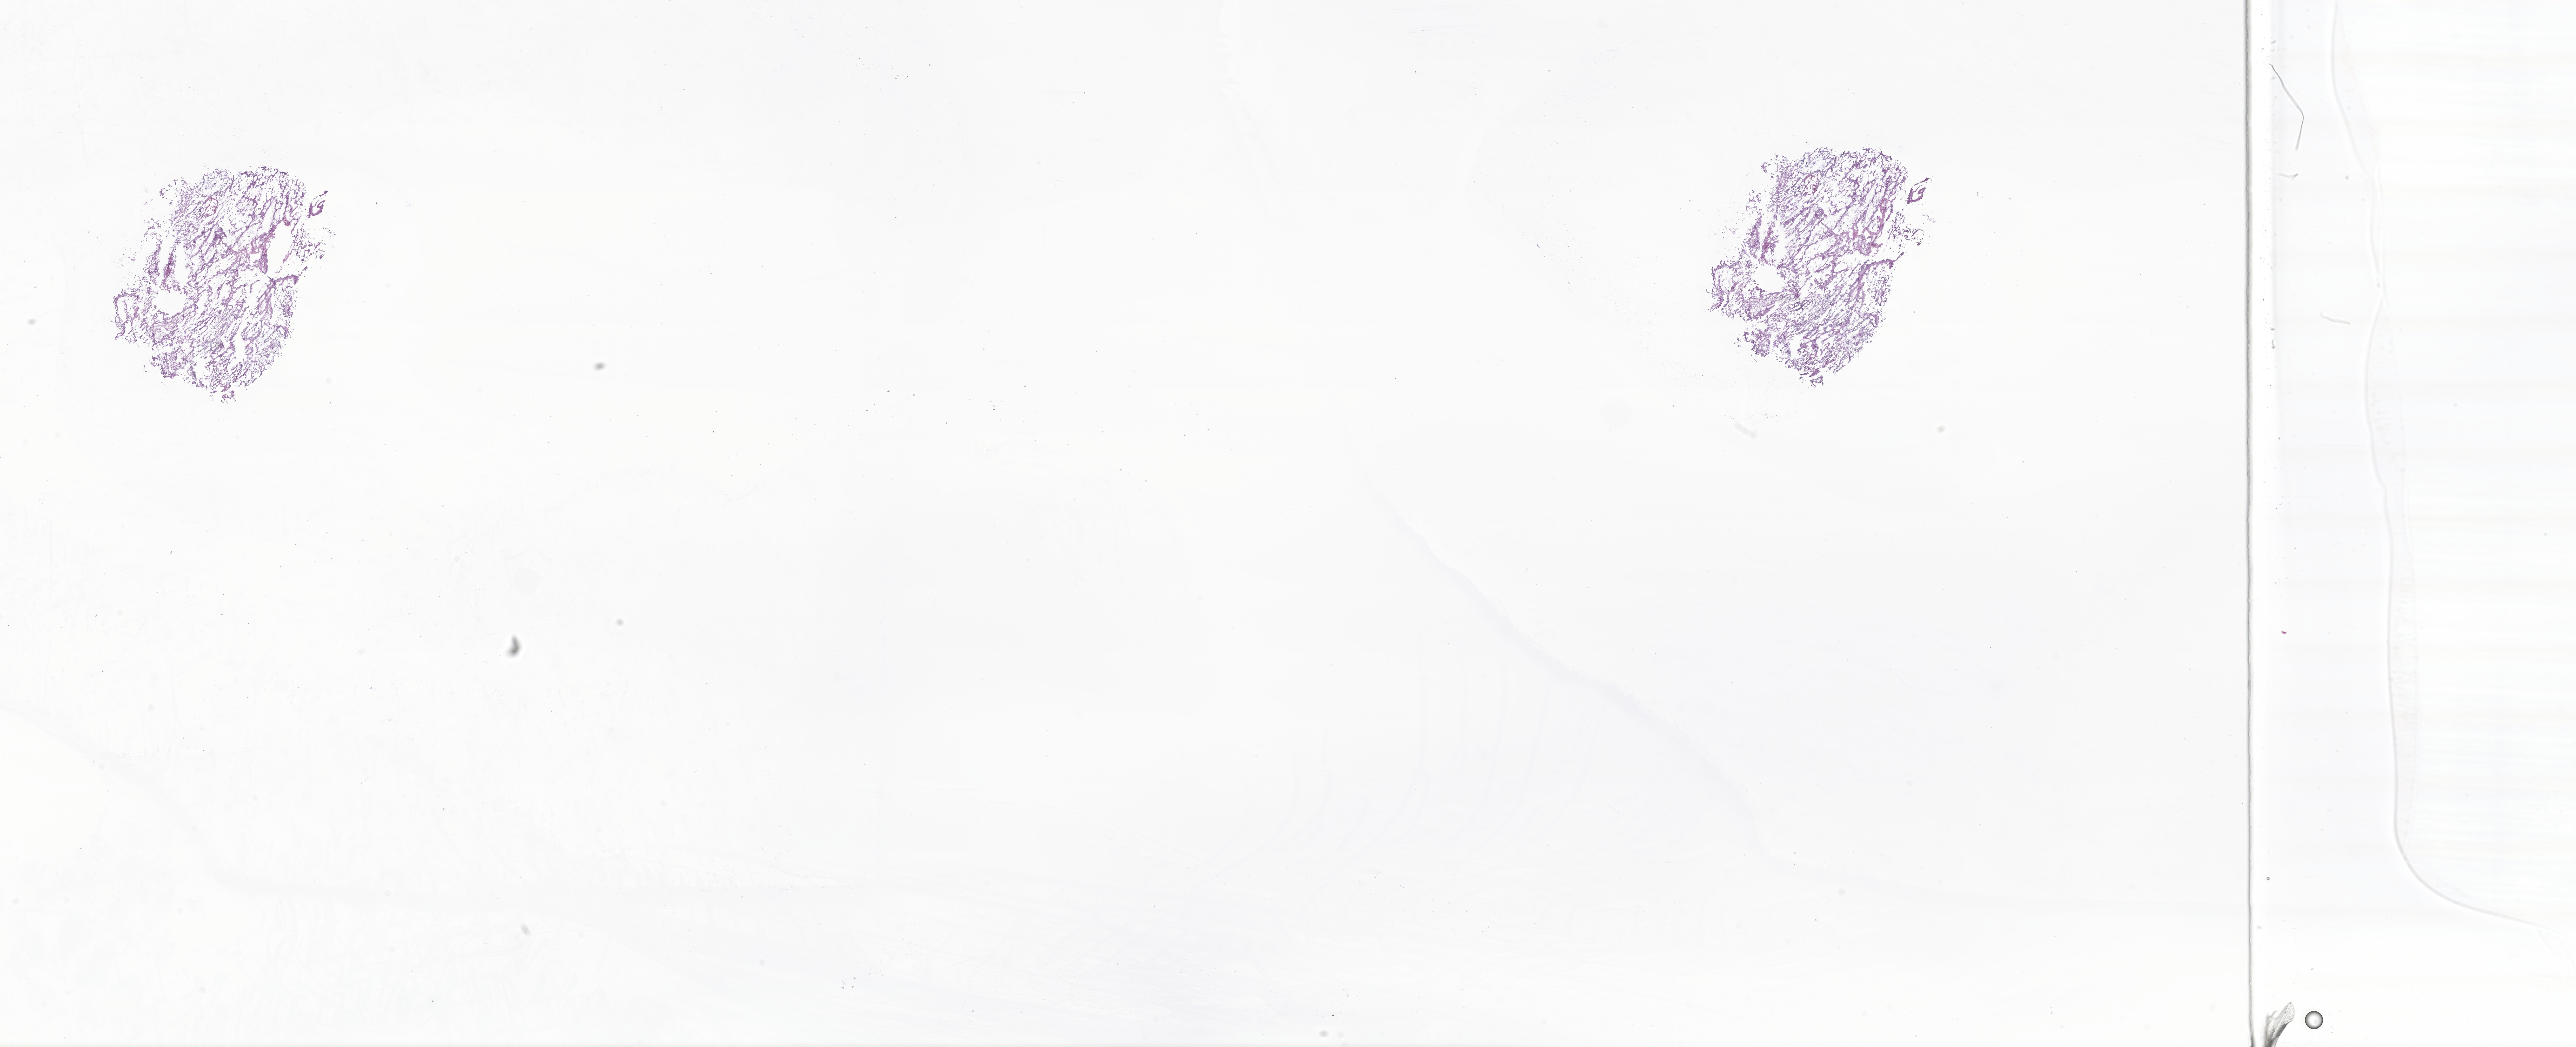
Whole-slide image, haematoxylin and eosin stain of tumor tissue from the cerebral ventricle, a low-resolution overview of the entire scanned area, about 41.8 x 17.0 mm. Frozen section (OCT-embedded). Female patient, age 644 days (about 1.8 years).
Diagnosis: Ependymoma, NOS.